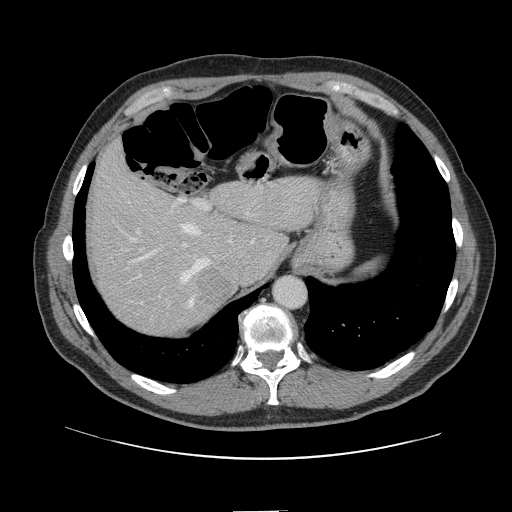
Contrast-enhanced abdominal CT, one axial slice. Slice 109 of 161 in the series (ordered by position). Intravenous contrast given. Soft-tissue window (W 400 / L 40 HU). 512 × 512 image matrix. Male patient, age 66 years. Case-level facts recorded for this patient, not image findings: diagnosis: colorectal cancer liver metastases, imaged before liver resection; multiple liver metastases: no; largest metastasis: 3.5 cm.
Outlined on this slice (manually delineated by an expert):
- hepatic veins: box from (x=127, y=212) to (x=249, y=308) px
- liver: (x=91, y=147)–(x=316, y=334)
- planned liver remnant (the part of the liver to remain after resection): (x=91, y=147)–(x=316, y=306)
- portal vein (with intrahepatic branches): (x=119, y=198)–(x=210, y=298)
- liver metastasis: (x=198, y=268)–(x=231, y=306)